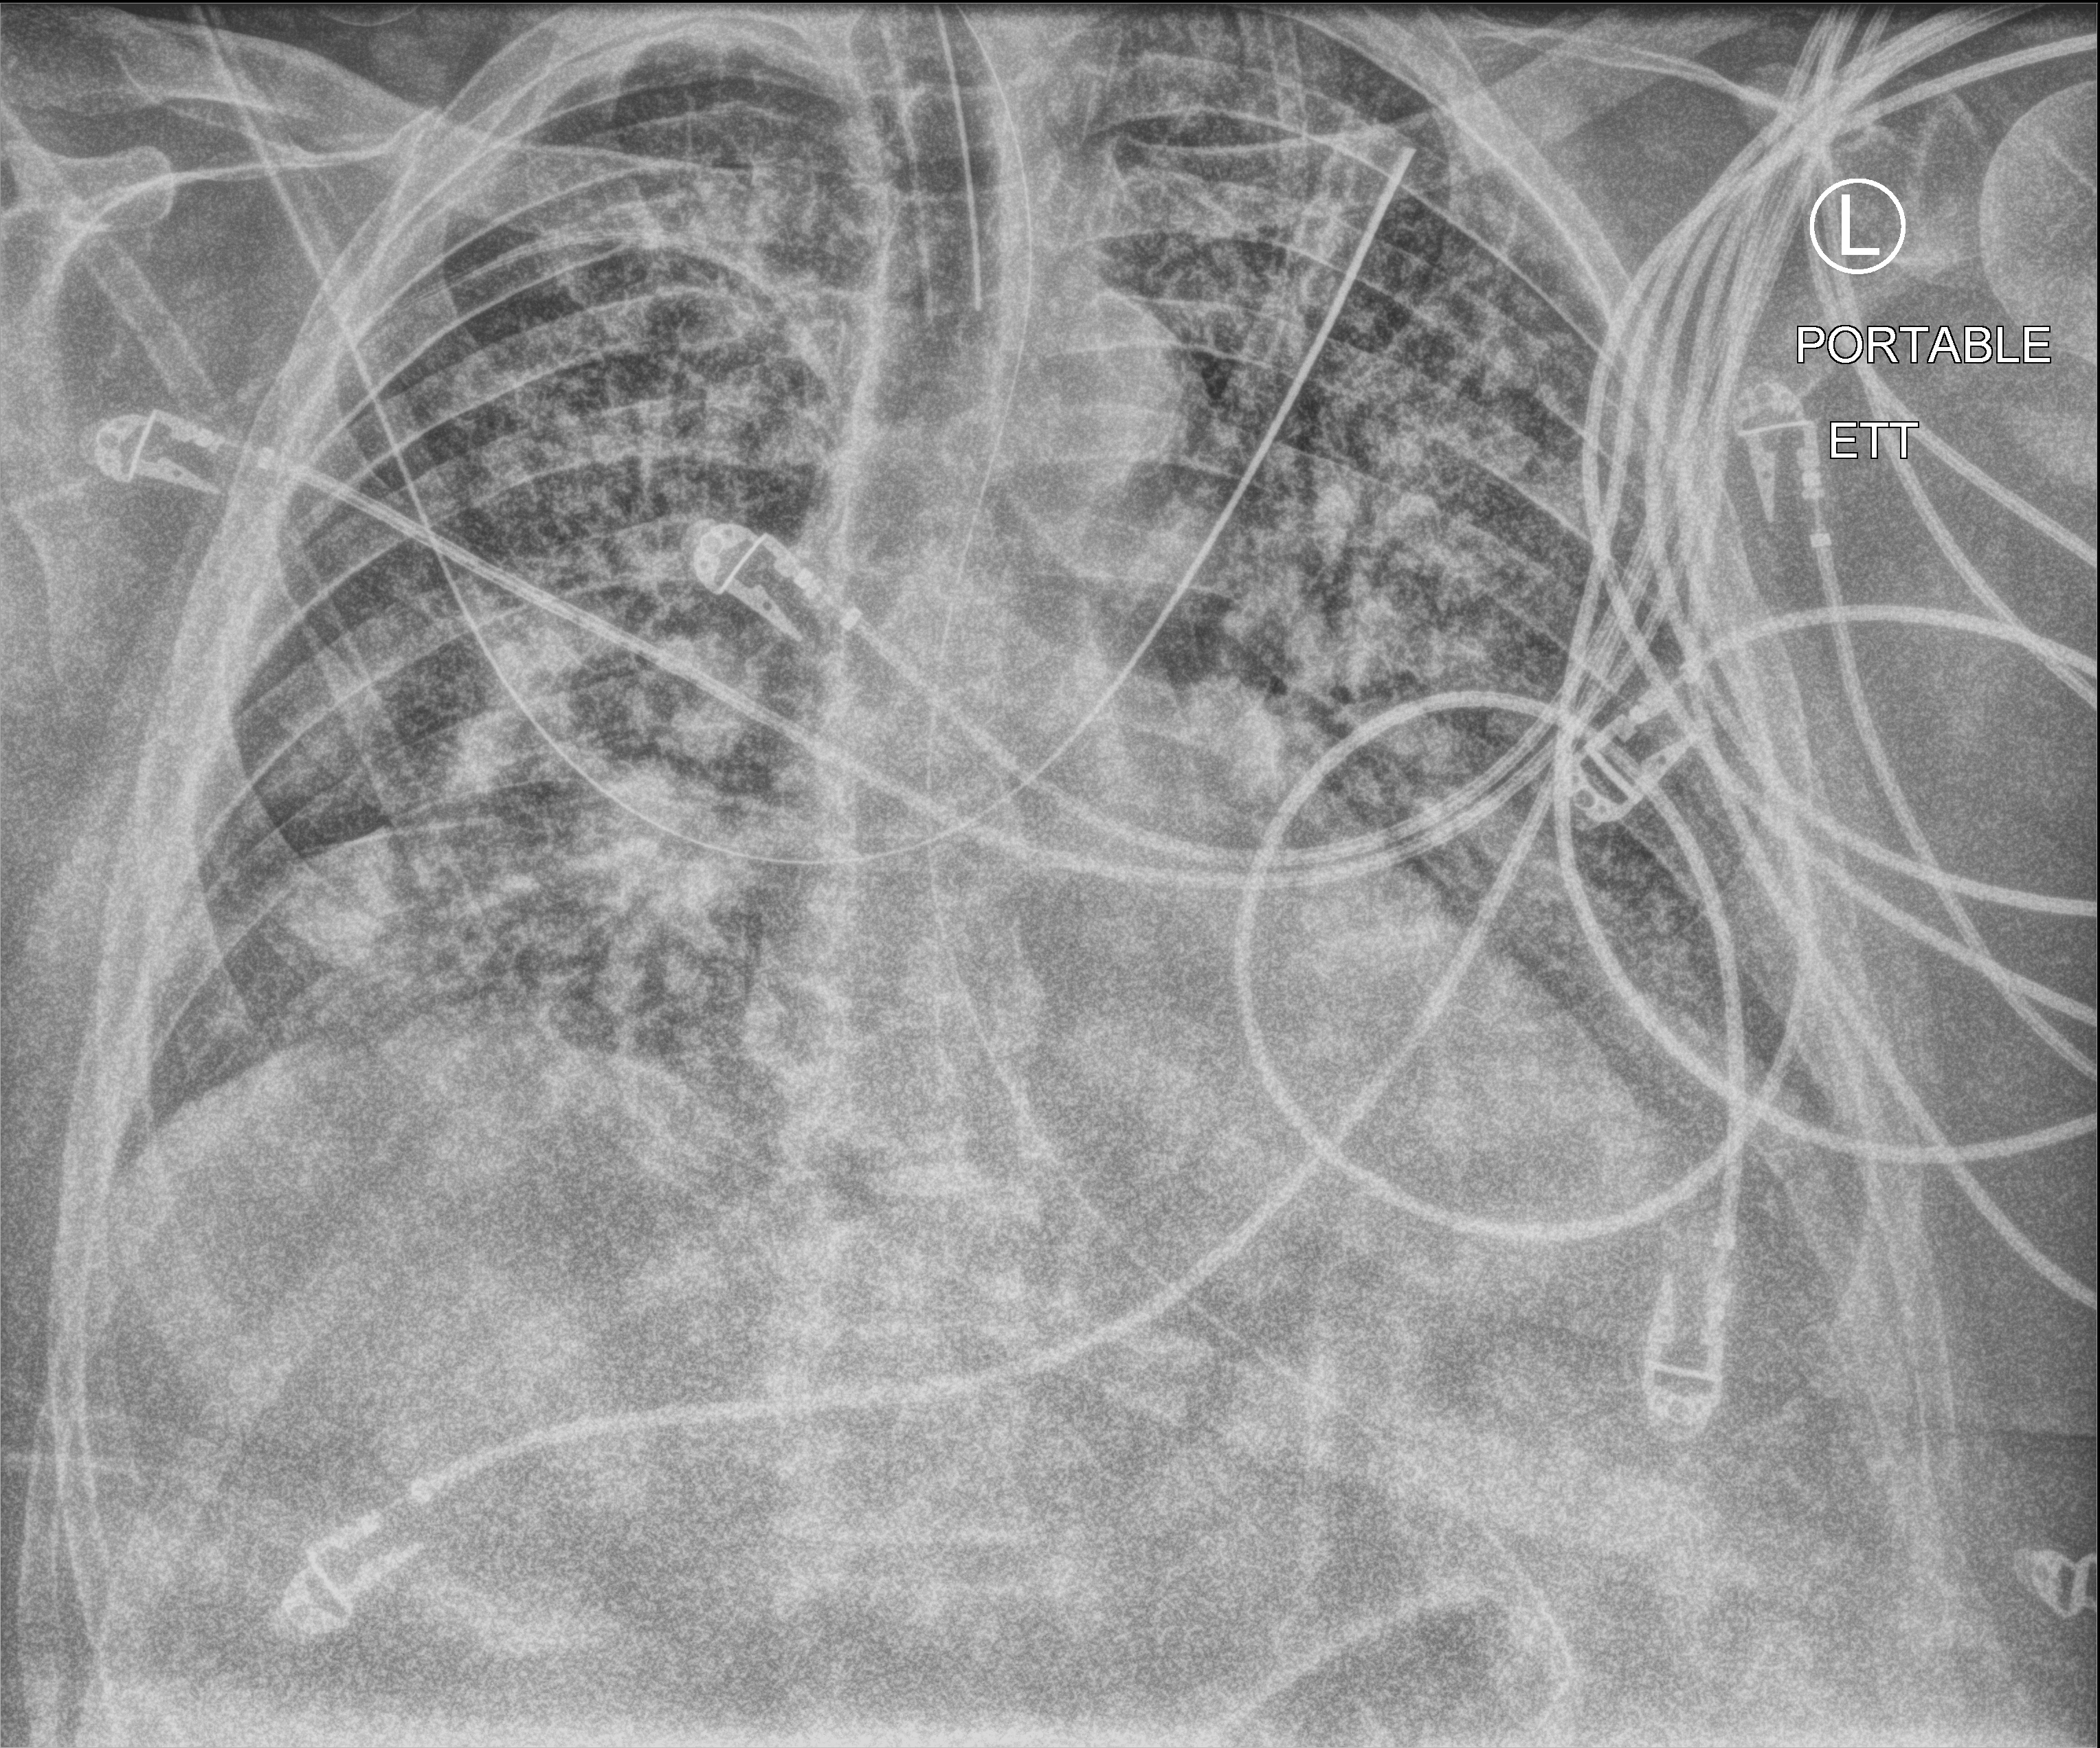
Bedside chest radiograph (computed radiography); anteroposterior (AP) projection. Patient hospitalised with COVID-19; male, aged 60–74 years.
Admission-level facts for this patient (not findings on this image; timing relative to this image not recorded):
- mechanically ventilated during this hospital stay: yes